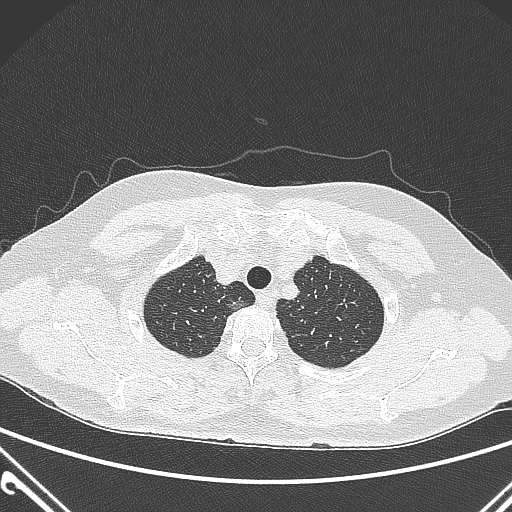
Chest CT, one axial slice; lung window (W 1500 / L -600 HU); 1 mm slice thickness; 512 × 512 image matrix. Patient: female, 54 years. From the clinical record (not read from this slice): clinical TNM (as recorded): T1a N0 M0; histopathological grade: G1.
Structures marked on this image (rectangle marked by the reading radiologist):
- lung tumour (recorded histology: adenocarcinoma): bounding box <222,292,249,321> (left, top, right, bottom; pixels)